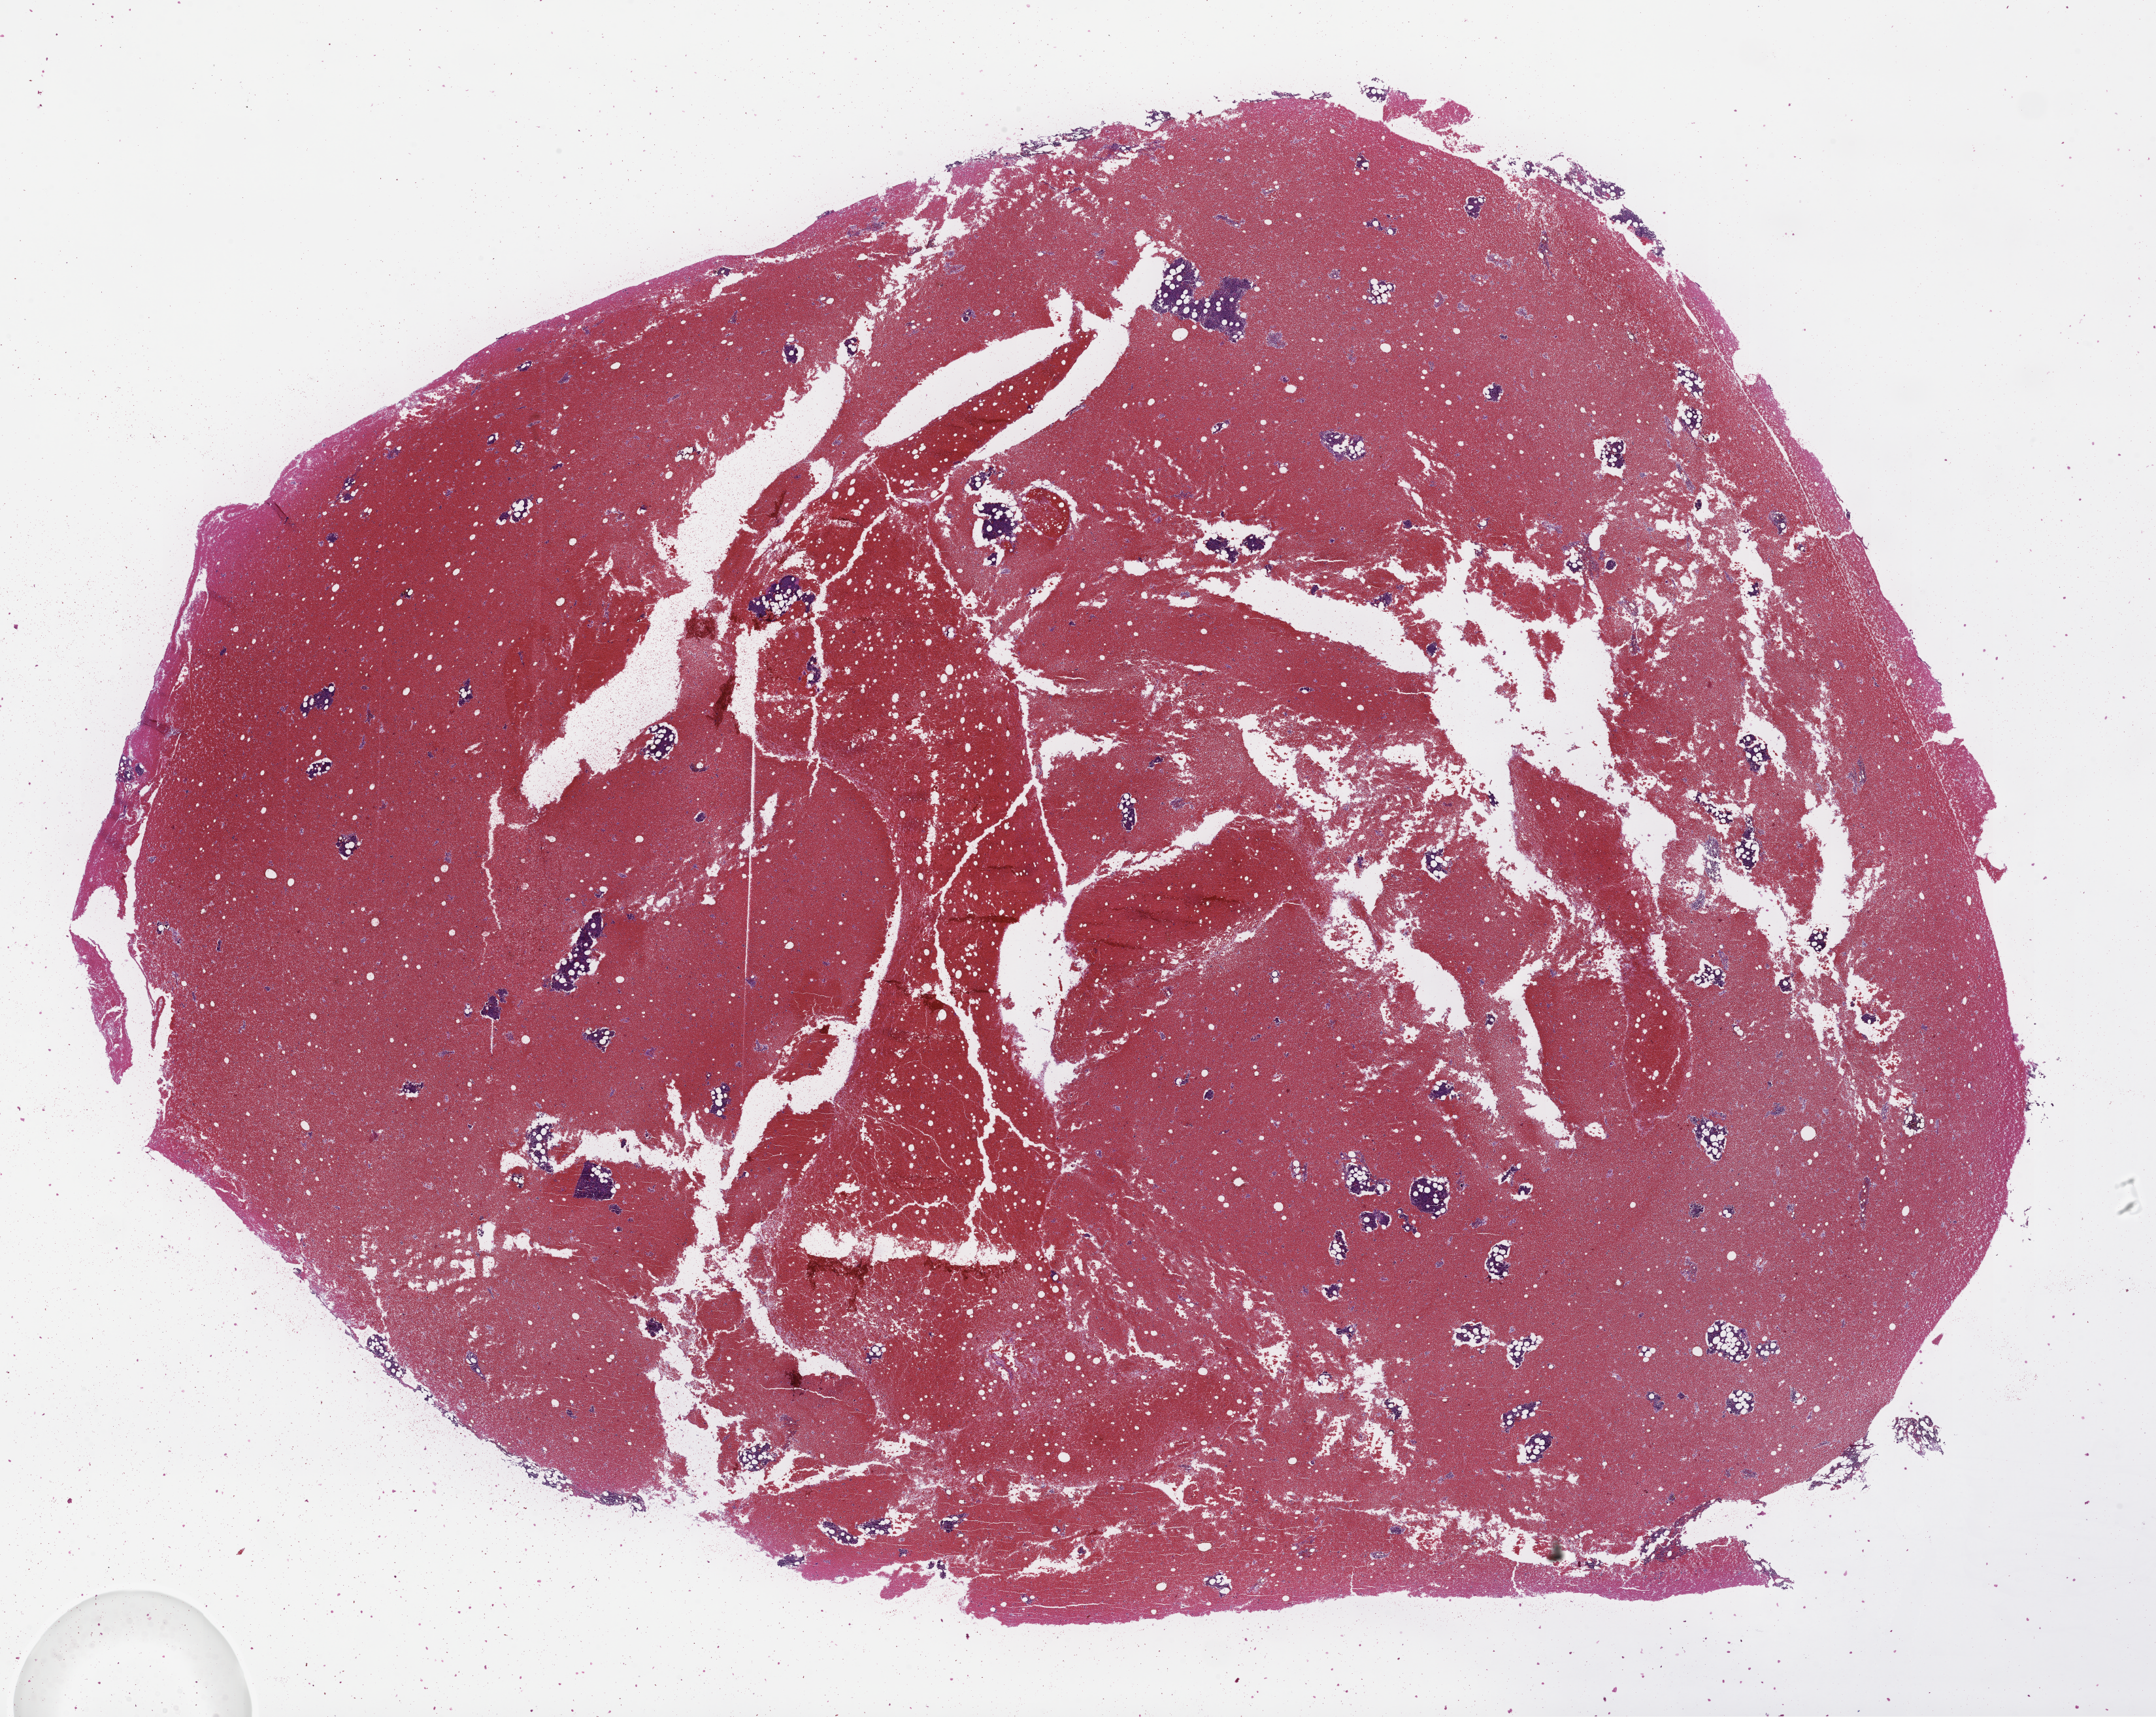
Digitized haematoxylin and eosin-stained section, low-resolution overview of the scanned area, about 26.6 x 21.2 mm; formalin-fixed paraffin-embedded section; tissue site: bone marrow. Patient sex: female.
This section: primary tumor. Diagnosis: Plasma Cell Myeloma.